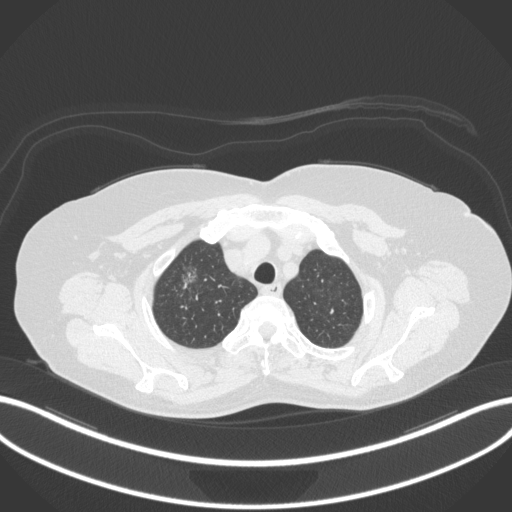
Chest CT, one axial slice. Position 299 of 365 along the scan axis. 120 kVp. Lung window (W 1500 / L -600 HU). 512 × 512 image matrix, field of view 400 × 400 mm. Female patient, age 62 years. From the clinical record (not read from this slice): clinical TNM (as recorded): T1c N0 M0.
Outlined on this slice (rectangle marked by the reading radiologist):
- lung tumour (recorded histology: adenocarcinoma): bounding box (x1, y1, x2, y2) in pixels: (174, 260, 202, 296)